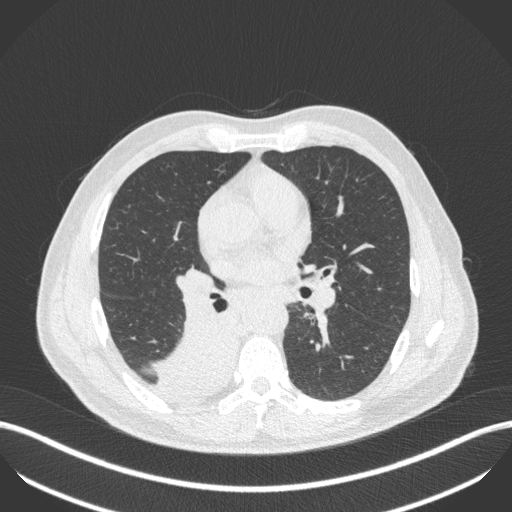
Chest CT, one axial slice. Position 254 of 451 along the scan axis. Reconstruction kernel B31f. Lung window (W 1500 / L -600 HU). 1 mm slice thickness. 512 × 512 image matrix, field of view 400 × 400 mm. Patient: male, 61 years. From the clinical record (not read from this slice): clinical TNM (as recorded): T1 N0 M0.
Outlined on this slice (rectangle marked by the reading radiologist):
- lung tumour (recorded histology: small cell carcinoma): bounding box <146,308,236,396> (left, top, right, bottom; pixels)